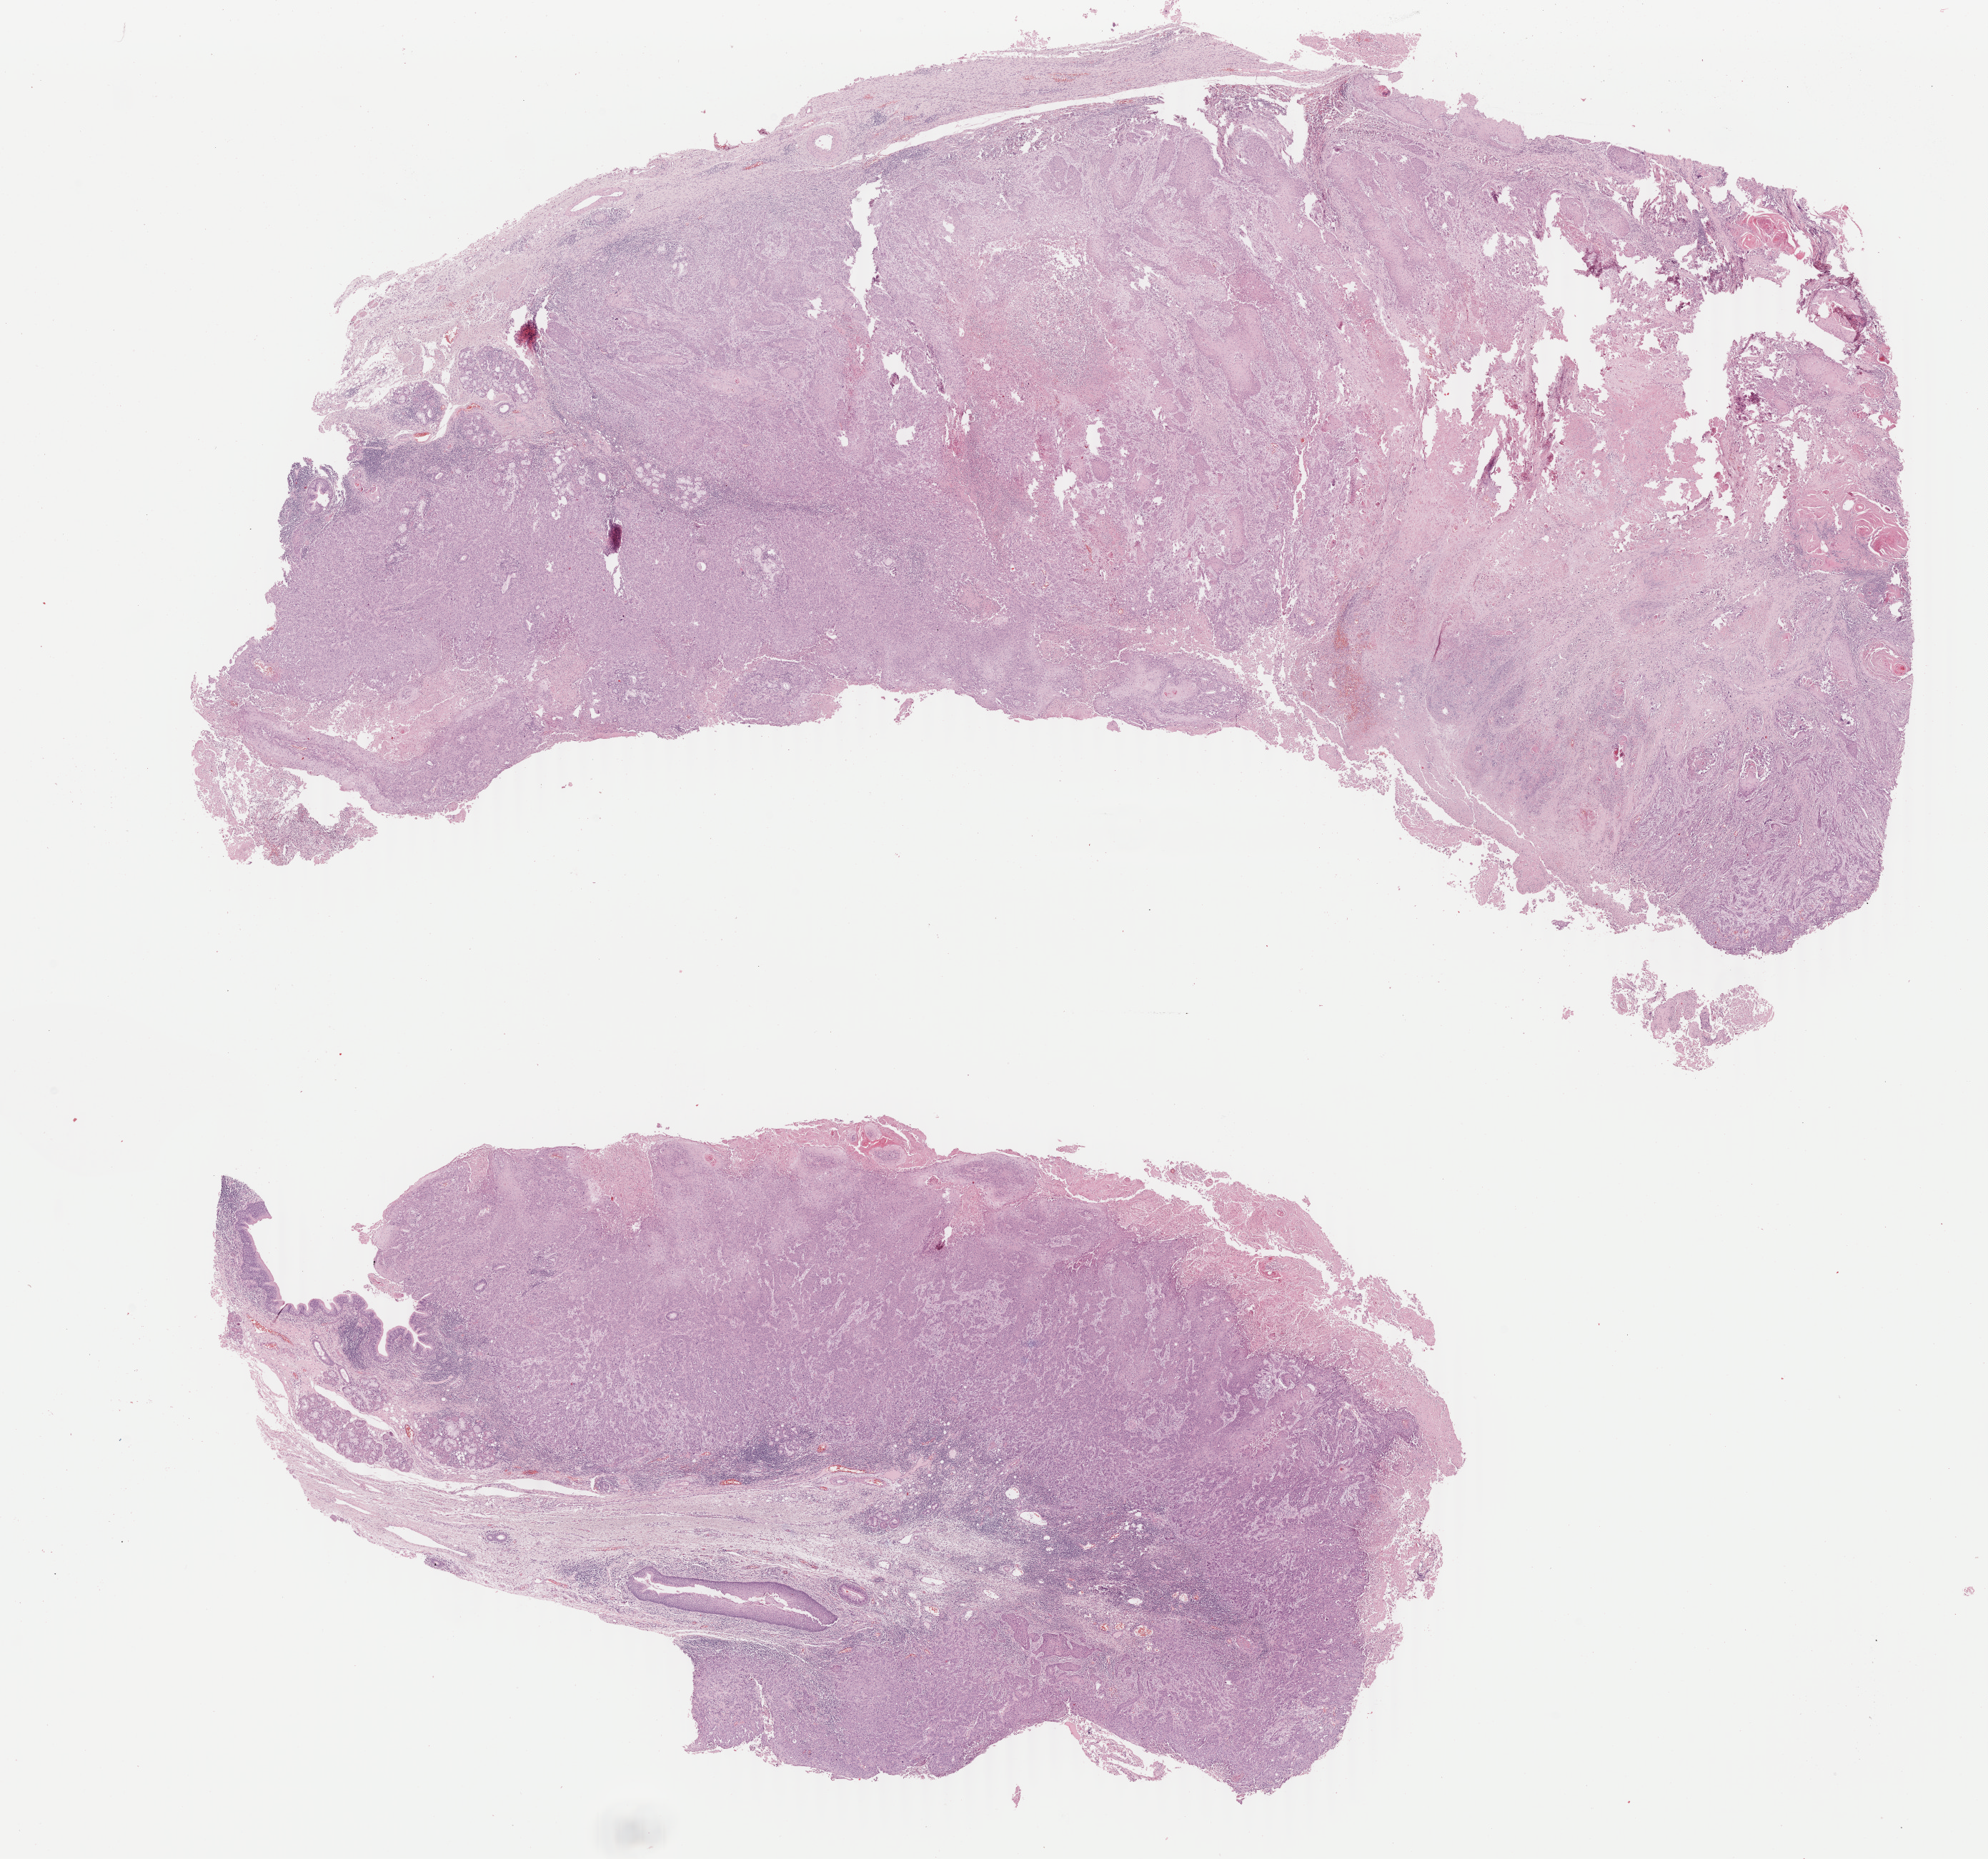
Hematoxylin and eosin (H&E) stained whole-slide image — shown as a low-resolution overview of the whole scanned area (about 22.1 x 20.7 mm, slide scanned at 40x); FFPE section; sample: primary tumour, head and neck. Patient: male, age at initial diagnosis 59 years. Histologic grade: G2 (moderately differentiated).
TNM: T3 N0. Laterality: midline. AJCC pathologic stage: III. Pathologic diagnosis: Squamous cell carcinoma, NOS (larynx, NOS).